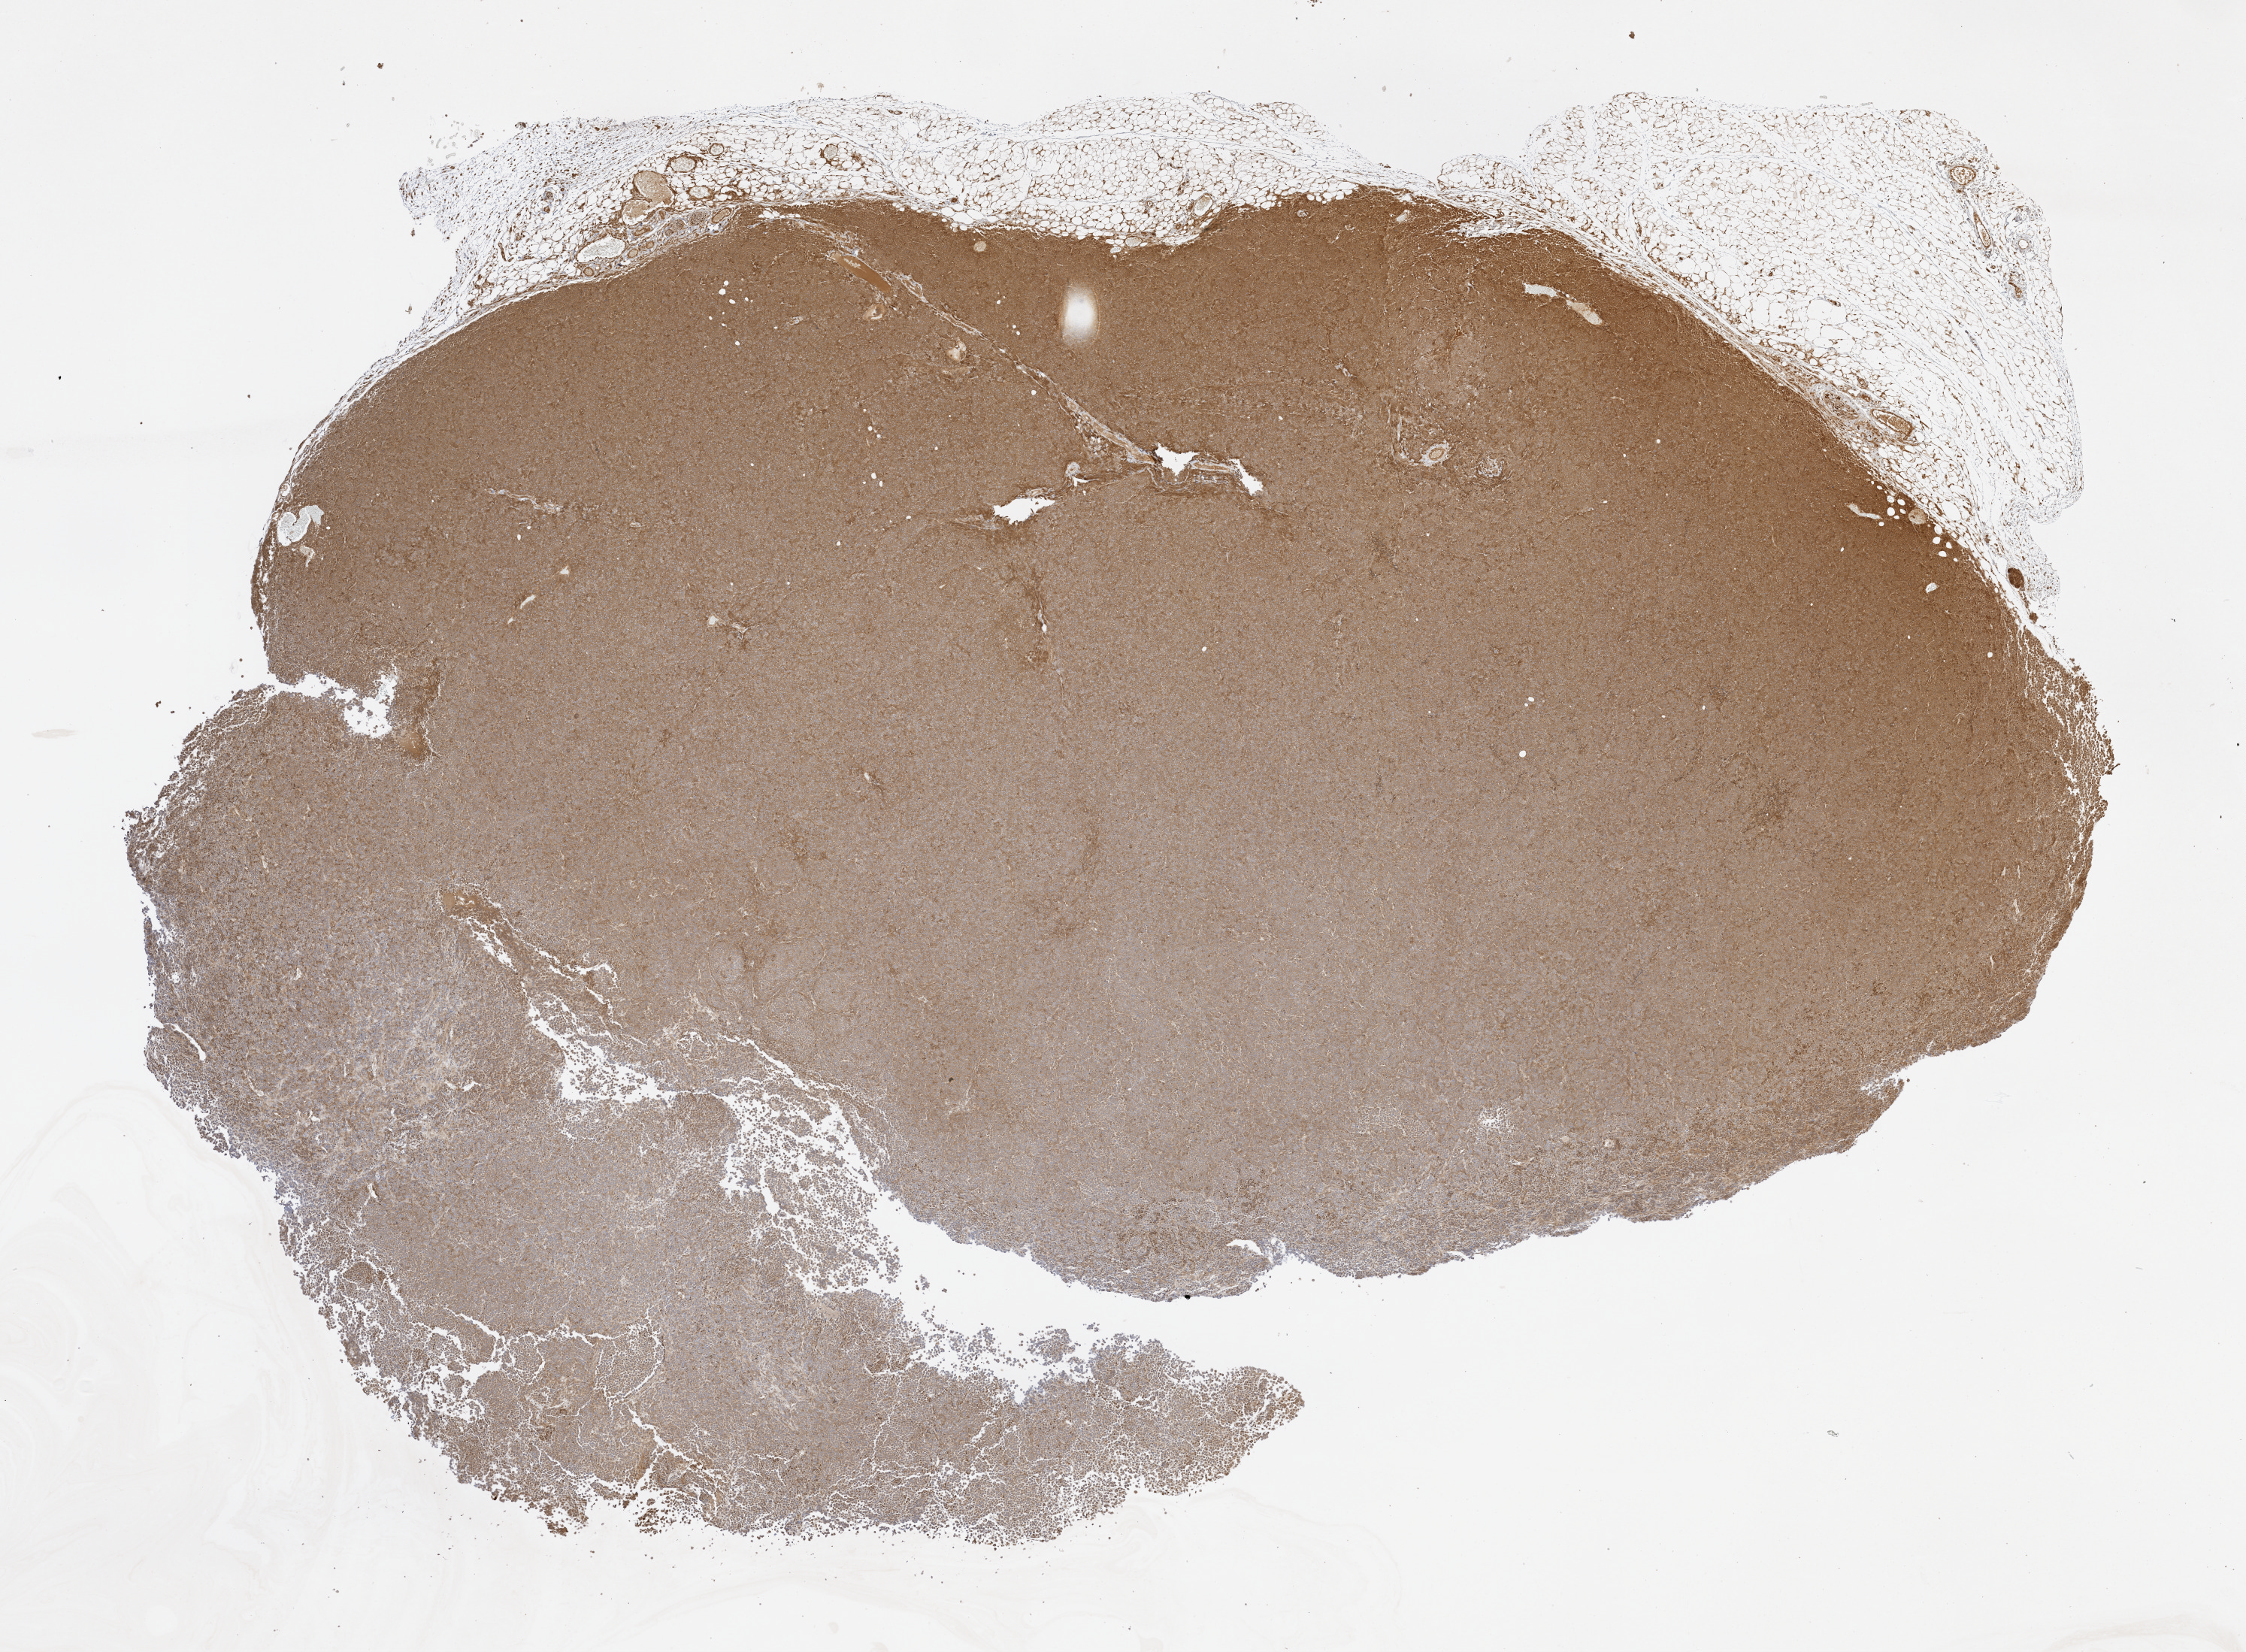
Whole-slide image, H&E: patient-derived xenograft (human tumor grown in a mouse), passage 0, whole scanned area (about 12.0 x 8.8 mm) shown as a low-resolution overview, formalin-fixed, paraffin-embedded (FFPE) tissue, originating tumor site category: endocrine.
Originating patient diagnosis: Merkel Cell Carcinoma.